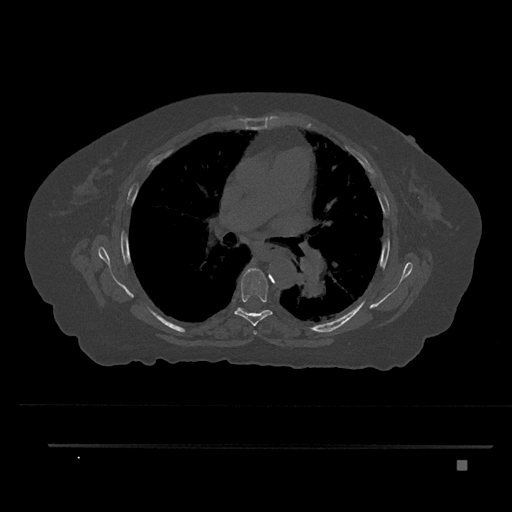
CT including the spine, one axial slice. Position 527 of 797 along the scan axis. Reconstruction kernel Br40s/3. 120 kVp. Bone window (W 1800 / L 400 HU). 512 × 512 image matrix, field of view 437 × 437 mm. Female patient, age 76 years. Case-level facts recorded for this patient, not image findings: primary cancer: lung; vertebrae with lytic lesions (as recorded): T11, L3.
Outlined on this slice (semi-automatically segmented with operator editing):
- T5 vertebra: bounding box <251,268,257,335> (left, top, right, bottom; pixels)
- T6 vertebra: <234,268,273,326>
- T7 vertebra: <238,308,265,311>